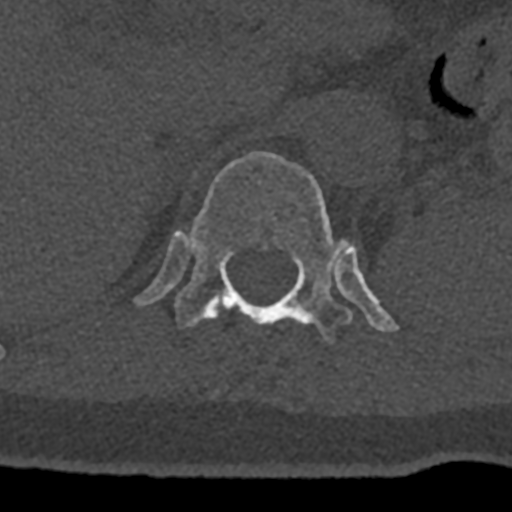
CT including the spine, one axial slice. Reconstruction kernel Br40s/3. Bone window (W 1800 / L 400 HU). 0.5 mm slice thickness. 512 × 512 image matrix, field of view 160 × 160 mm. Patient: male, 74 years. Case-level facts recorded for this patient, not image findings: primary cancer: renal.
Annotated regions visible in this slice (semi-automatically segmented with operator editing):
- T11 vertebra: bounding box <216,309,219,314> (left, top, right, bottom; pixels)
- T12 vertebra: <135,151,397,344>